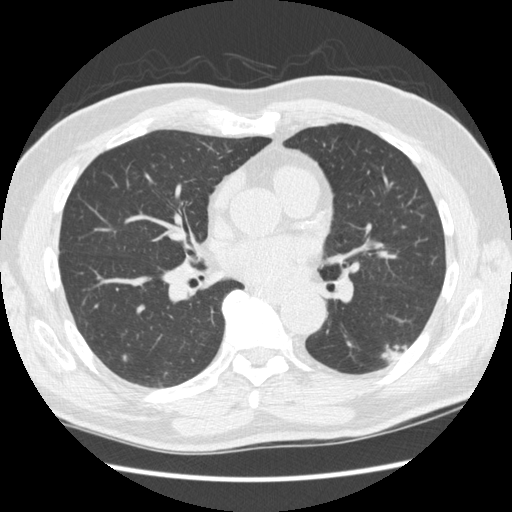
Chest CT (low-dose screening protocol), one axial image; baseline annual screen; lung window (W 1500 / L -600 HU); standard (soft-tissue) reconstruction kernel (STANDARD); slice 129 of 267 in the series; 512 × 512 image matrix, field of view 360 × 360 mm. Male participant, aged 74 years at enrolment. Former smoker at enrolment.
- Lesion marked by an expert reader, bounding box <375,324,417,374> (left, top, right, bottom; pixels).
- The screening reader recorded 3 non-calcified nodules or masses ≥4 mm on this exam (right upper lobe, right lower lobe, left upper lobe); which of them this box marks is not recorded.
- Official screen result: positive, change unspecified: nodule(s) >= 4 mm or enlarging nodule(s), mass(es), or other non-specific abnormalities suspicious for lung cancer.
- Later outcome: lung cancer diagnosed 384 days after this screen — squamous cell carcinoma, NOS, left lower lobe, well differentiated (G1), stage IA (AJCC 6th edition), 28 mm at pathology.